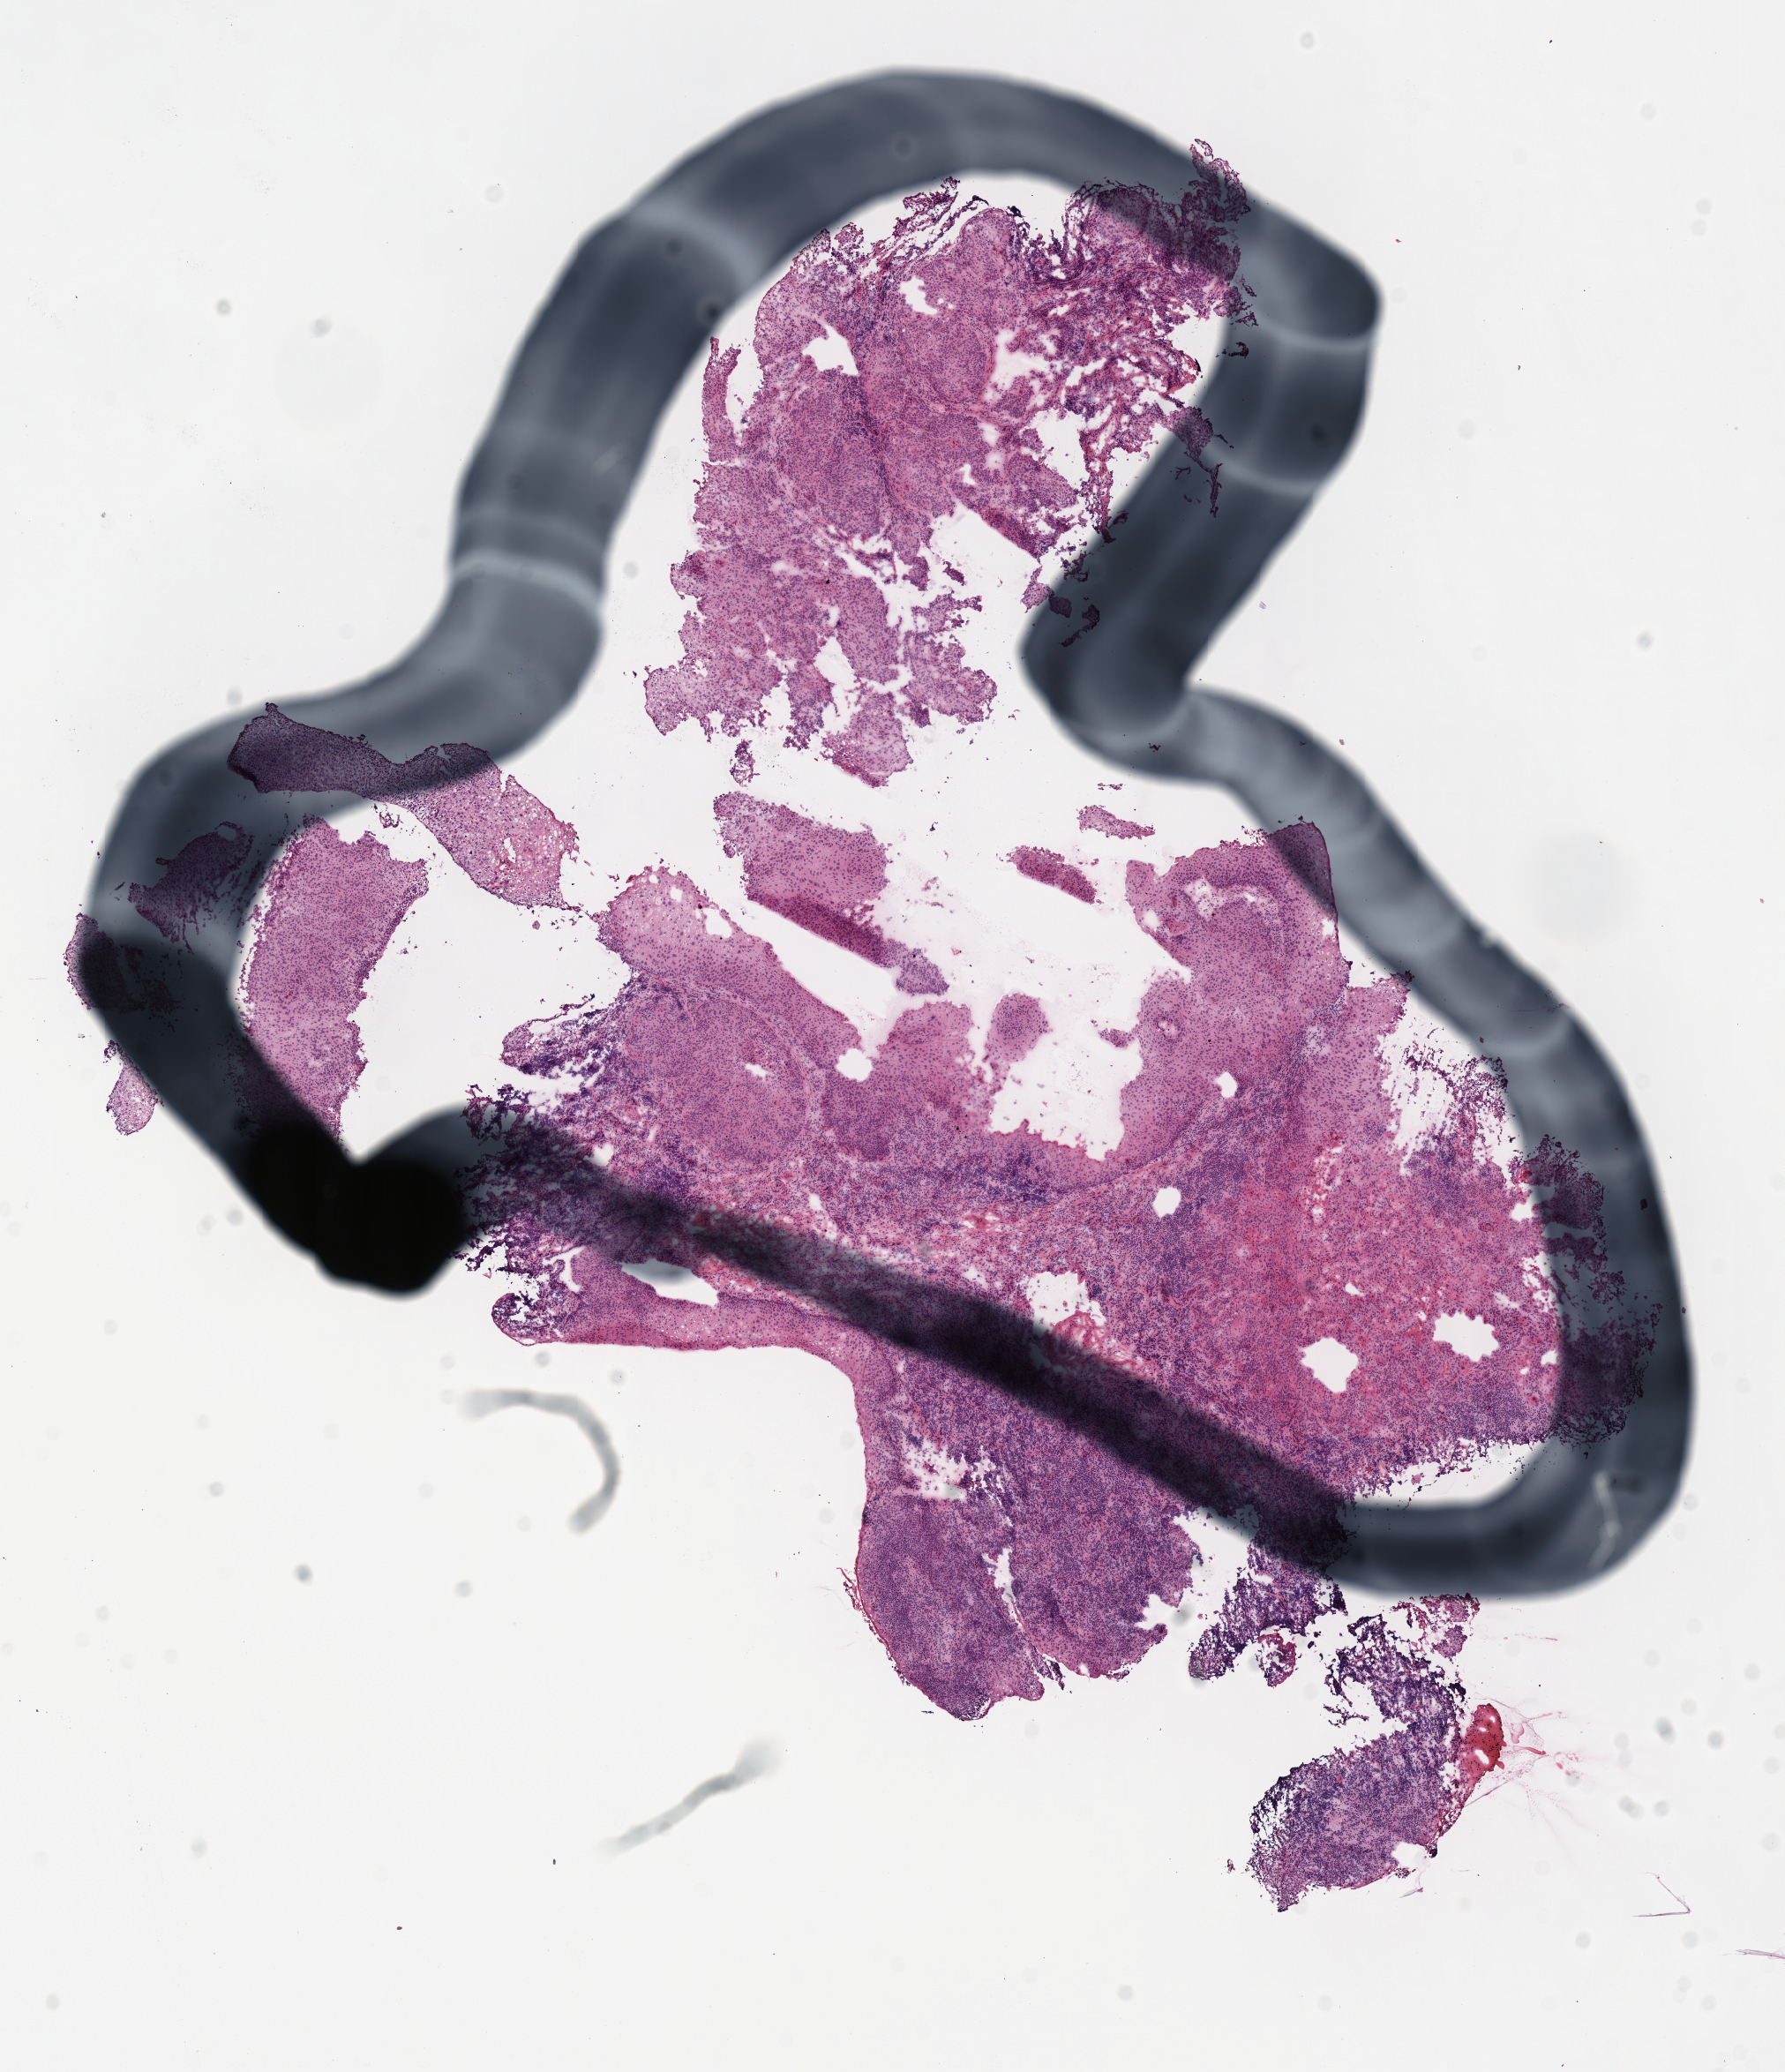
Digitized Hematoxylin and eosin (H&E) stained tissue section (whole slide), shown as a low-resolution overview of the whole scanned area (about 8.0 x 9.2 mm, from a 40x scan); frozen section; primary tumour sample from the head and neck. Patient: male, age at initial diagnosis 48 years. Histologic grade: G4 (undifferentiated). Slide review estimates, as recorded: tumour cells 75%, tumour nuclei 65%, normal cells 10%, stromal cells 15%, necrosis 0%. Inflammatory infiltration, as recorded: lymphocyte infiltration 25%.
Pathologic diagnosis: Squamous cell carcinoma, NOS.